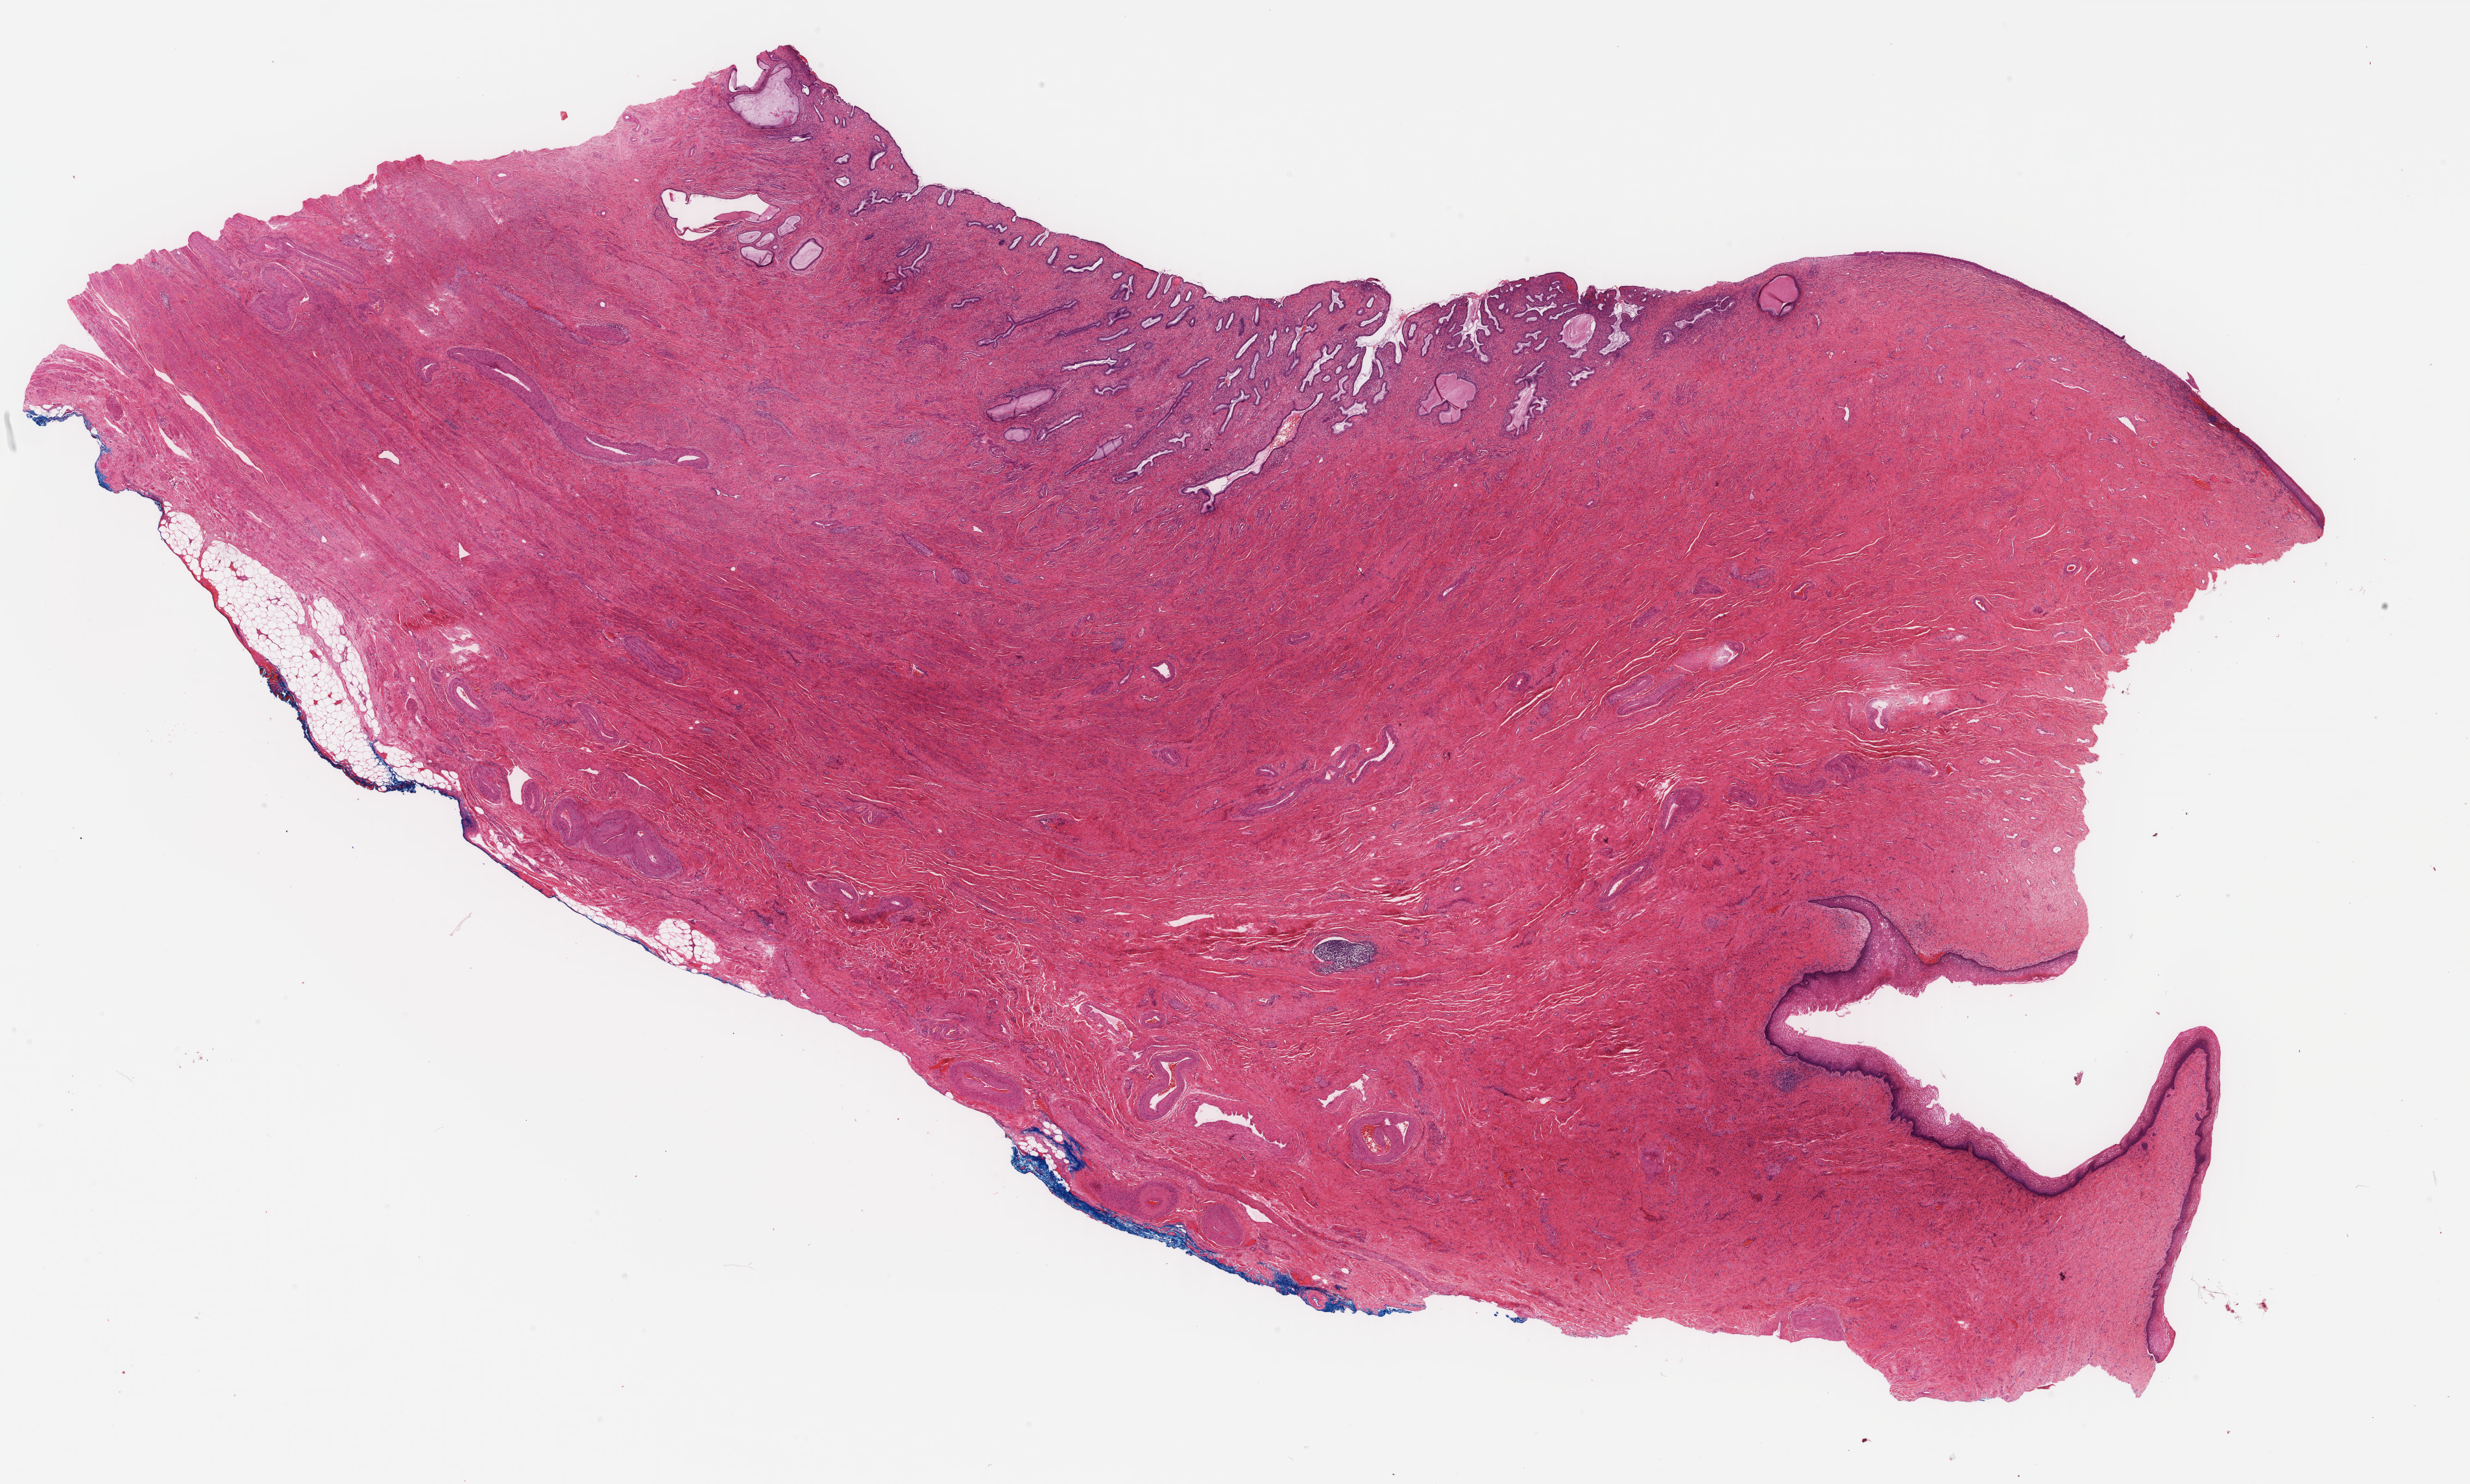
H&E whole-slide image — low-resolution overview of the scanned area, about 30.2 x 18.2 mm. Formalin-fixed paraffin-embedded (FFPE) diagnostic section. Primary tumour sample from the uterus. Female patient; age at initial diagnosis 64 years. Histologic grade: G3 (poorly differentiated).
• FIGO stage: IB
• lymph nodes positive (case pathology): 0 of 7 examined
• histologic diagnosis: Endometrioid adenocarcinoma, NOS (endometrium)